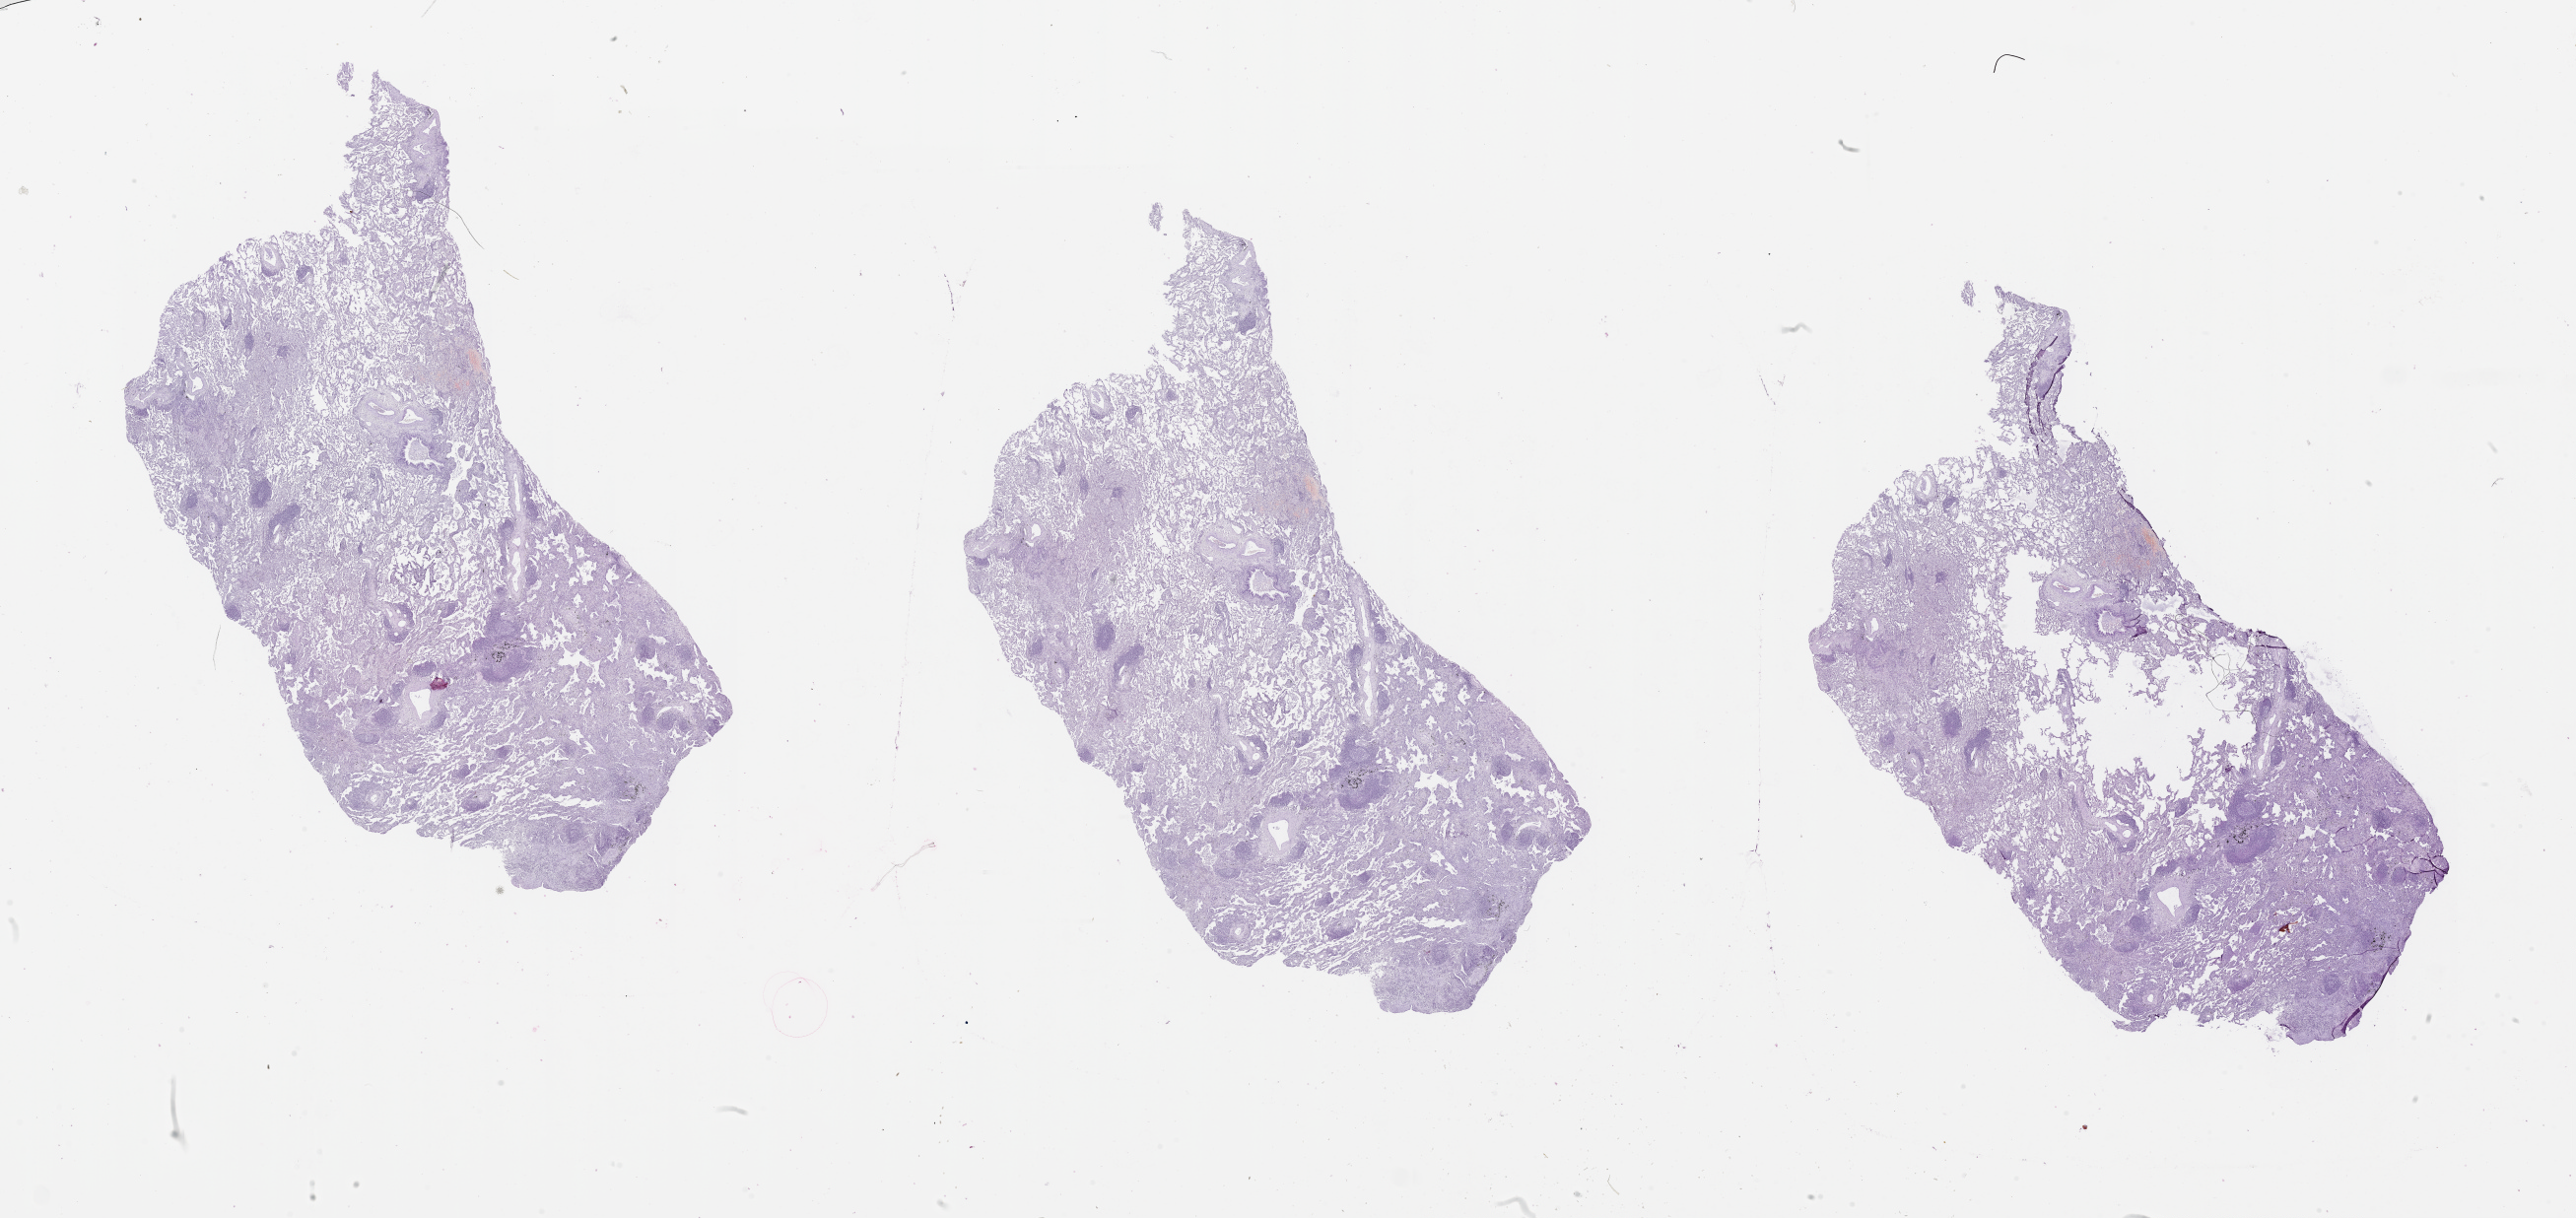
Digitized H&E-stained tissue section (whole slide), low-resolution overview of the scanned area, about 42.1 x 19.9 mm (acquisition: 20x scan); lung, tumour tissue. Patient: male, age 70 years.
• patient diagnosis (cohort enrolment): squamous cell carcinoma (lung)